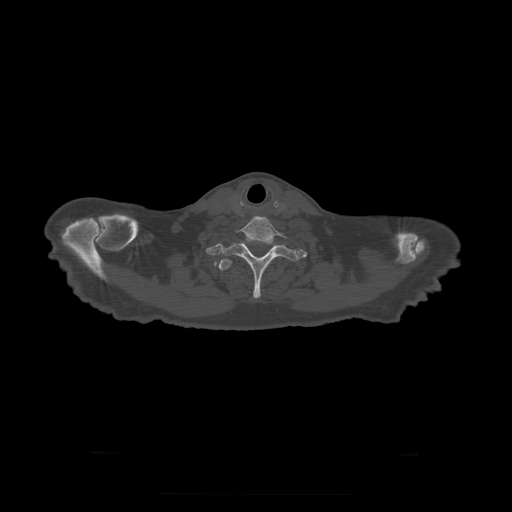
CT including the spine, one axial slice. Position 290 of 397 along the scan axis. Reconstruction kernel STANDARD. 120 kVp. Bone window (W 1800 / L 400 HU). 1.25 mm slice thickness. 512 × 512 image matrix. Patient age 73 years. From the clinical record (not read from this slice): primary cancer: prostate.
Structures marked on this image (semi-automatically segmented with operator editing):
- T1 vertebra: bounding box <221,237,298,299> (left, top, right, bottom; pixels)
- T2 vertebra: <220,259,233,271>